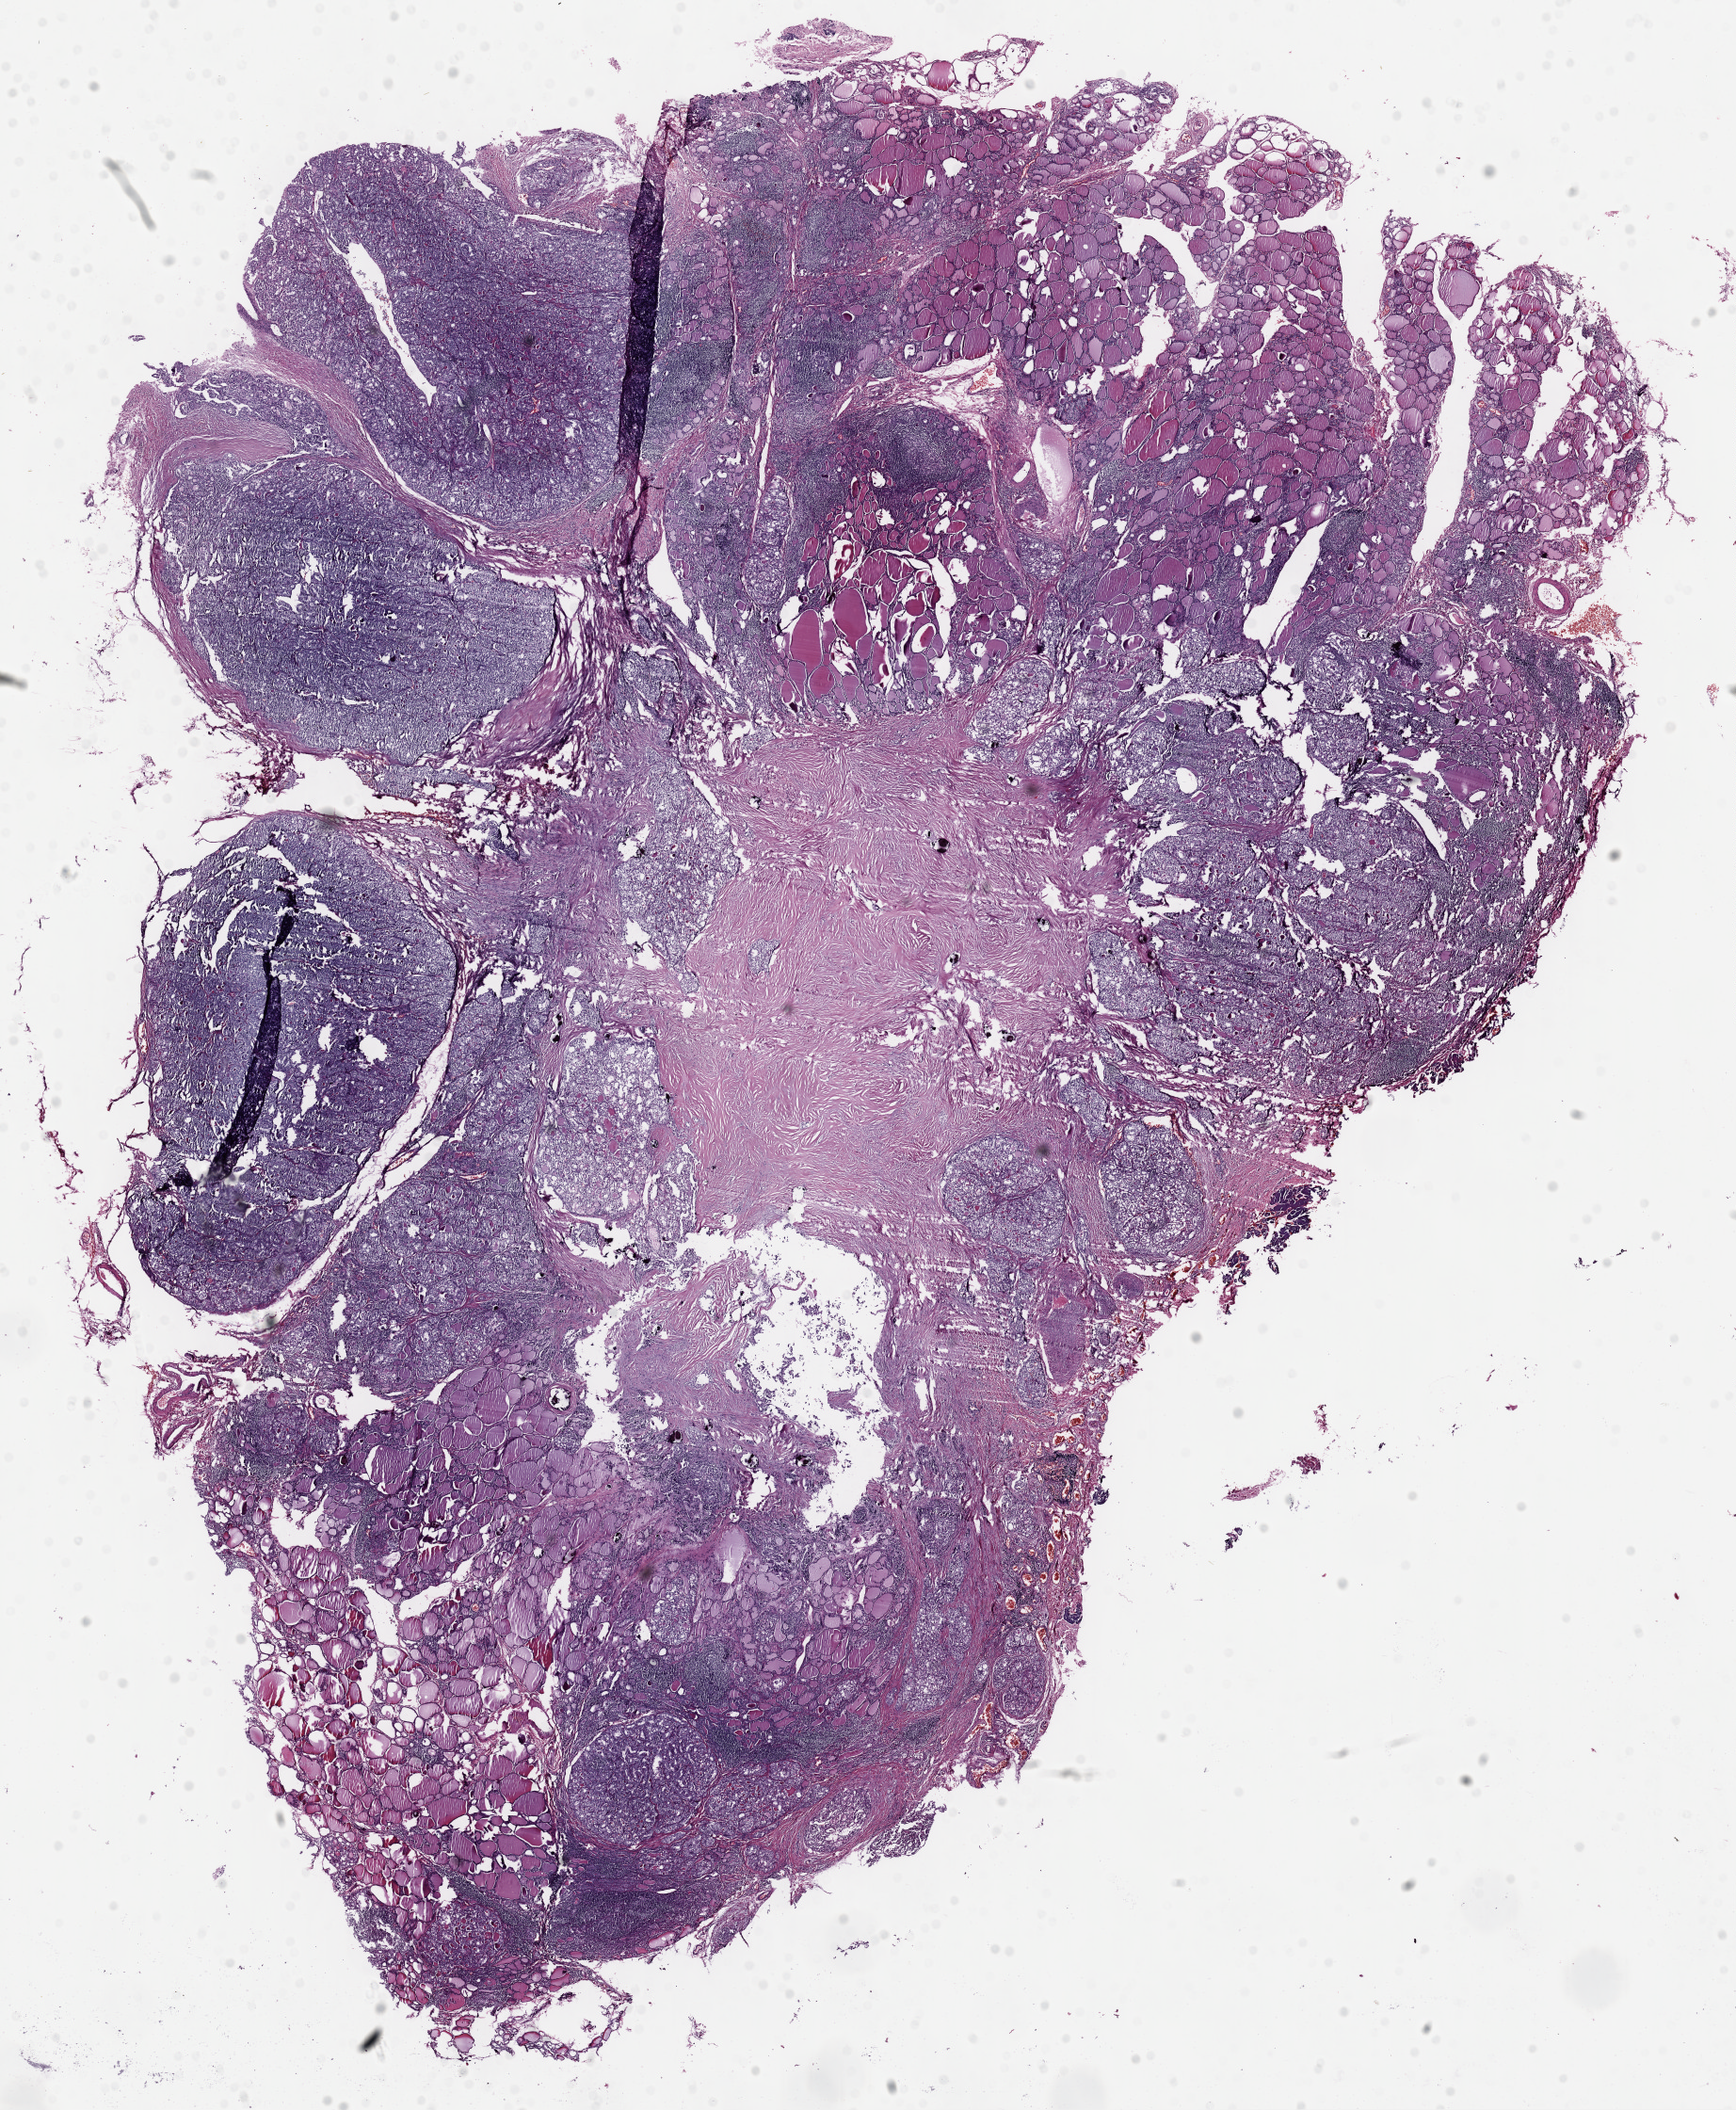
H&E whole-slide image, a low-resolution overview of the entire scanned area, about 14.6 x 17.7 mm (acquisition: 40x scan). Formalin-fixed paraffin-embedded (FFPE) diagnostic section. Primary tumour sample from the thyroid. Patient: female, age at initial diagnosis 28 years.
AJCC pathologic stage: I (6th edition). Diagnosis: Papillary adenocarcinoma, NOS.